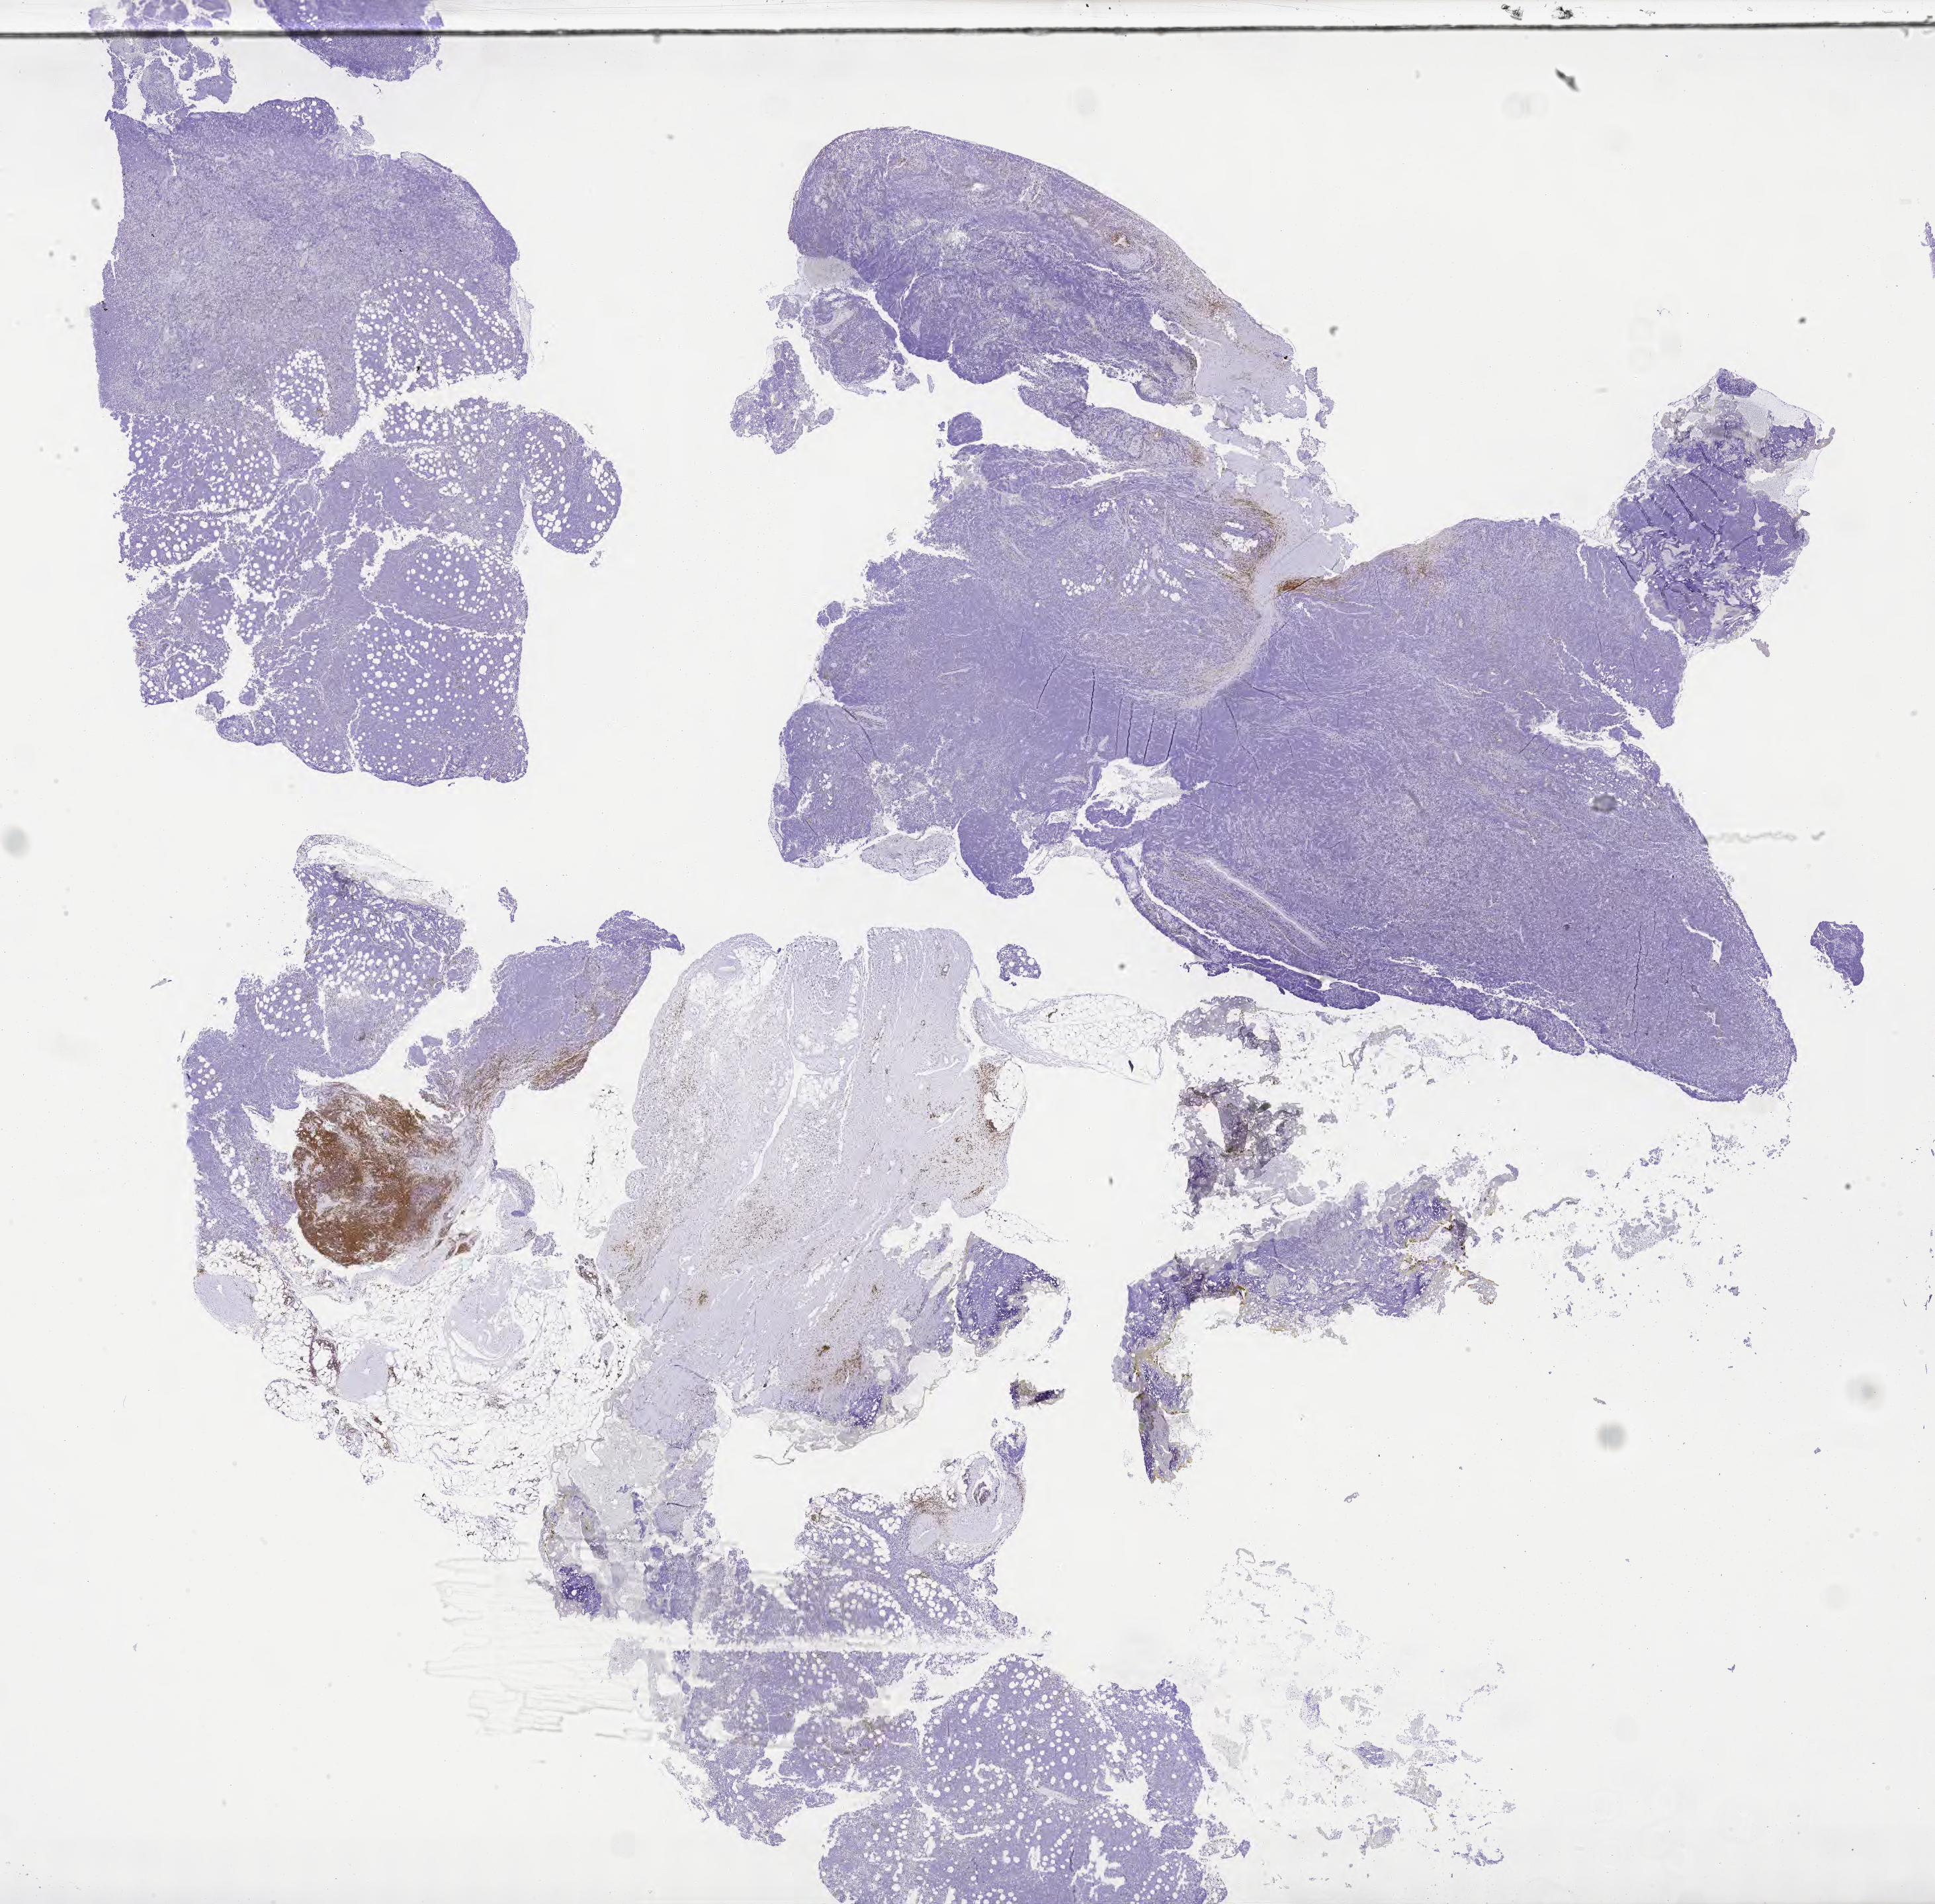
IHC for CD5, whole-slide image, shown as a low-resolution overview of the whole scanned area (about 23.6 x 23.3 mm), tumor tissue. Patient: female, age 72 years.
Diagnosis: Burkitt lymphoma, NOS.